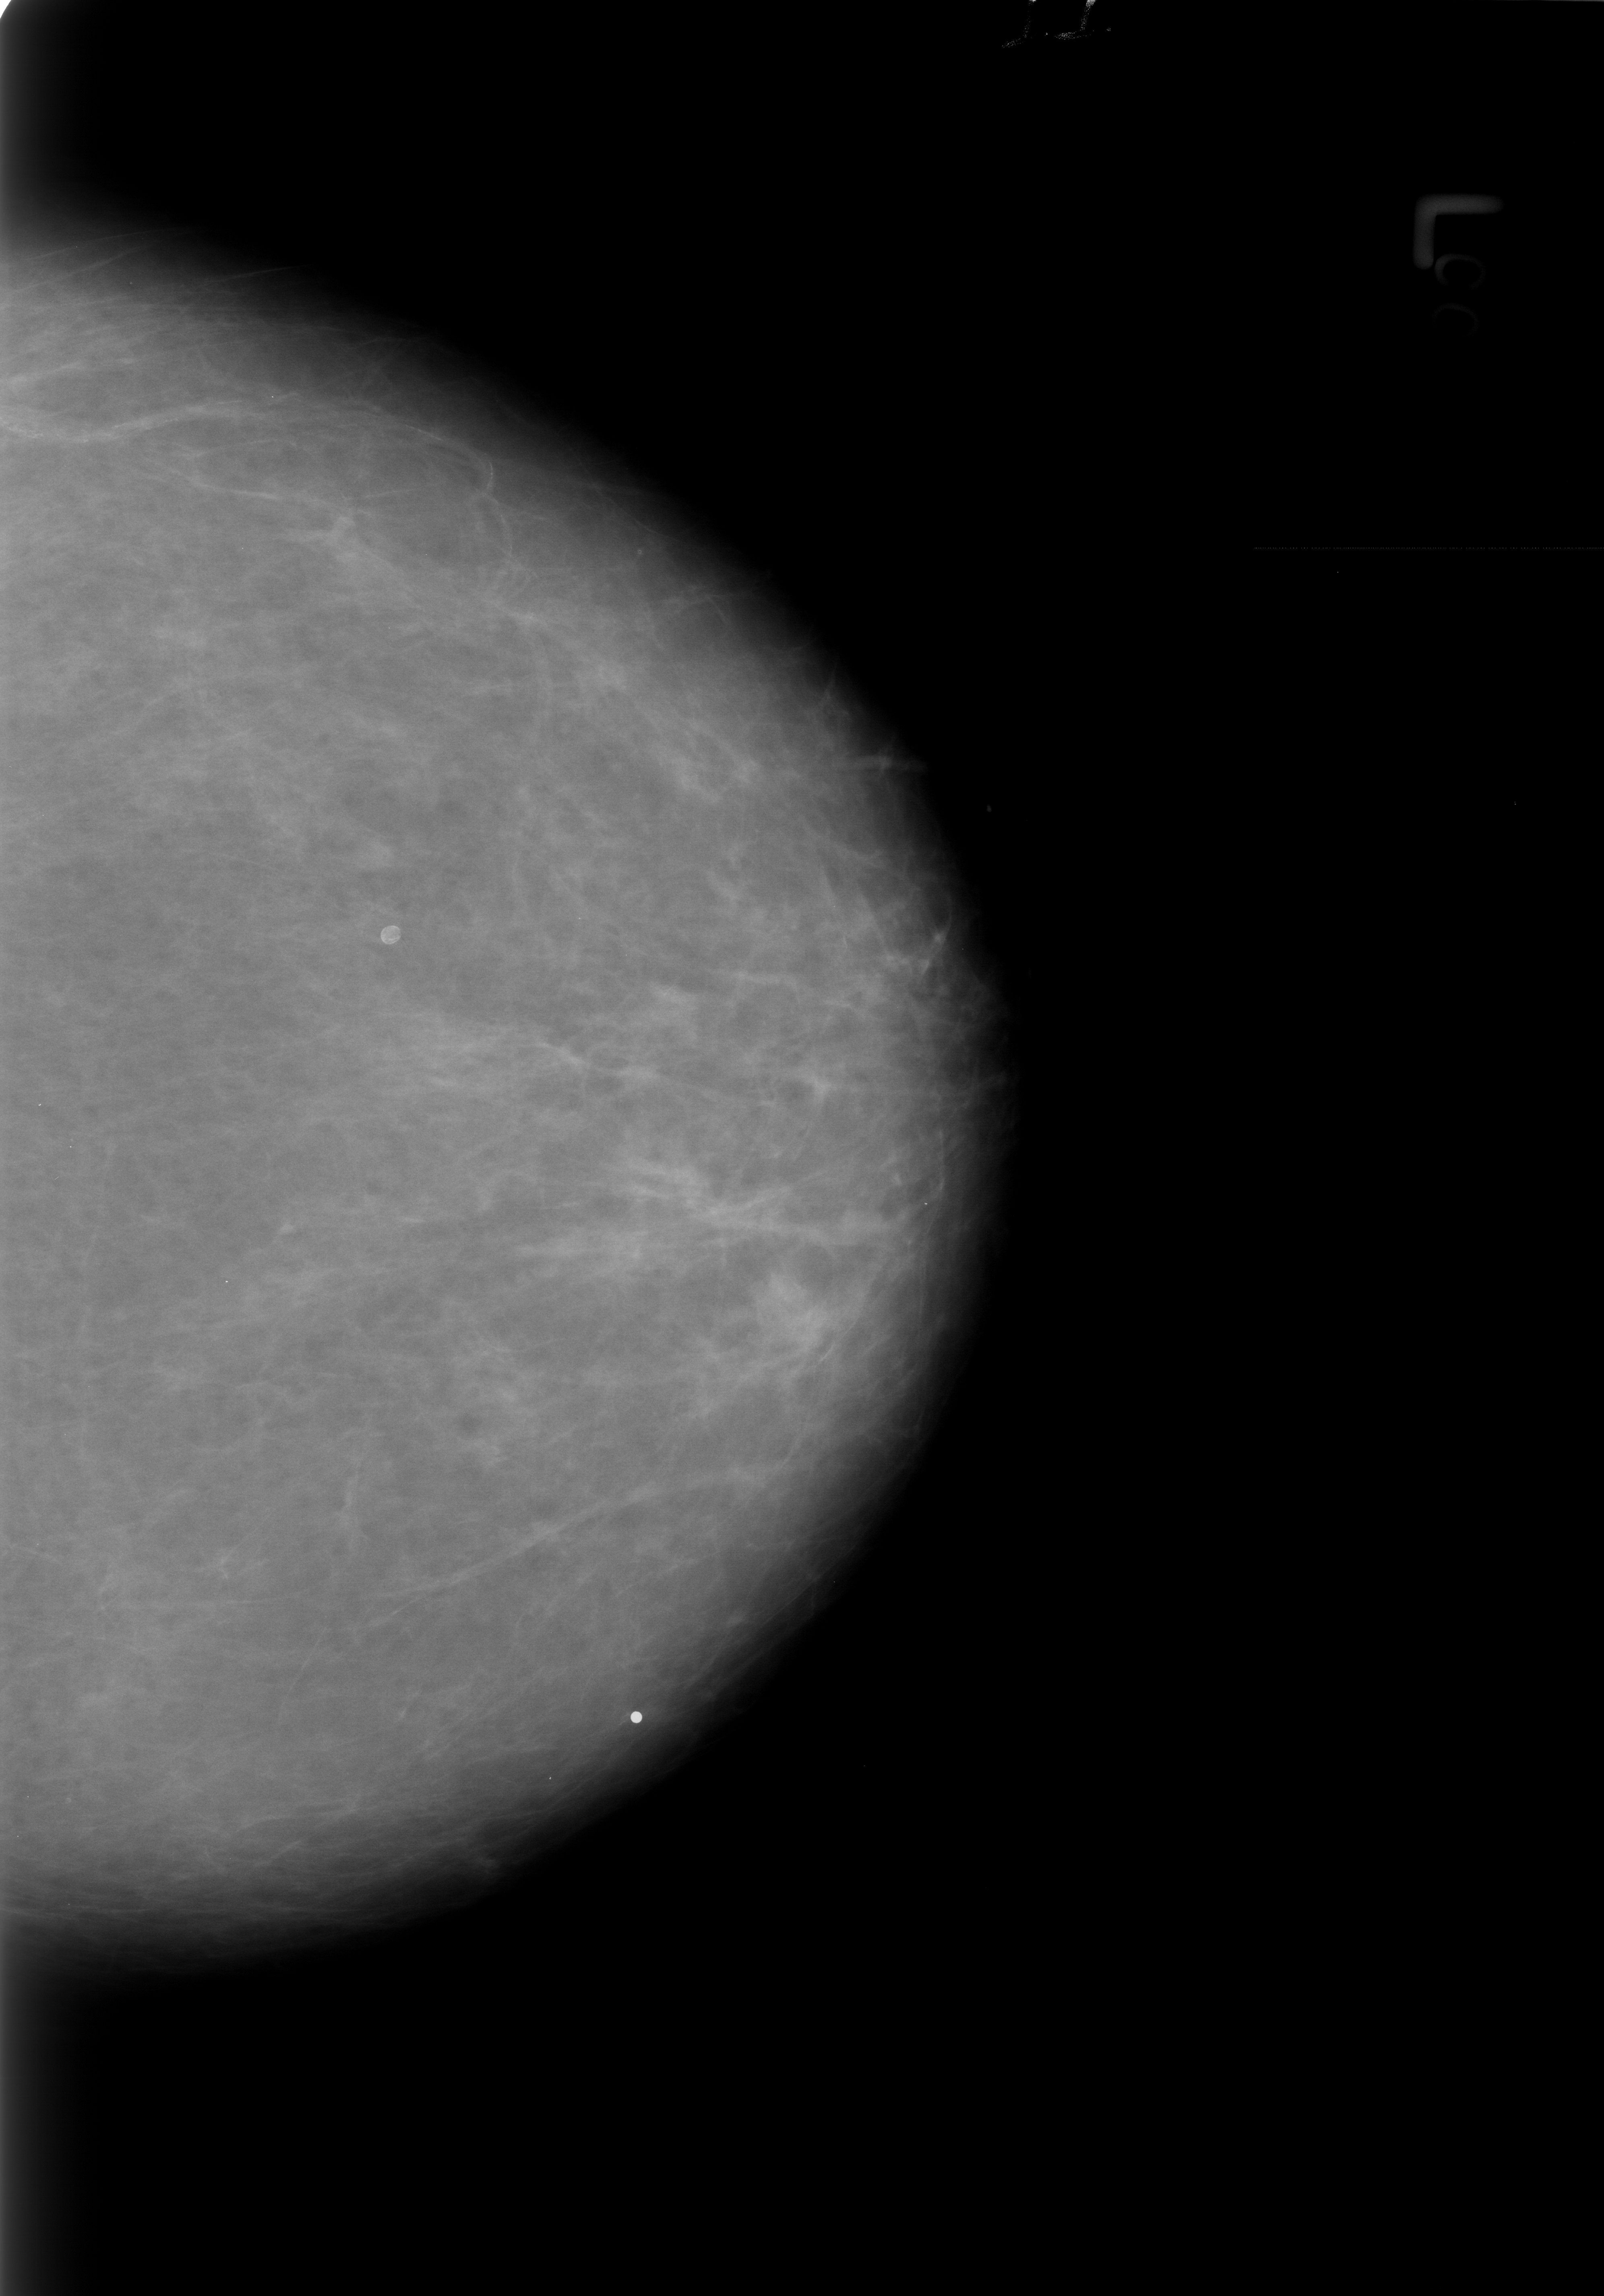
Mammogram (digitized film). Left breast. Craniocaudal (CC) view. Breast composition: almost entirely fatty (BI-RADS density category 1 of 4). 1604 × 2296 image matrix.
Expert-marked regions of interest on this film, with their recorded descriptors:
- calcifications, morphology lucent centered; BI-RADS assessment category 2; subtlety rating 3 on a 1 (subtle) to 5 (obvious) scale; outcome (as recorded, no biopsy): benign without callback (not worked up further): bounding box [x1, y1, x2, y2] px = [370, 911, 413, 954]